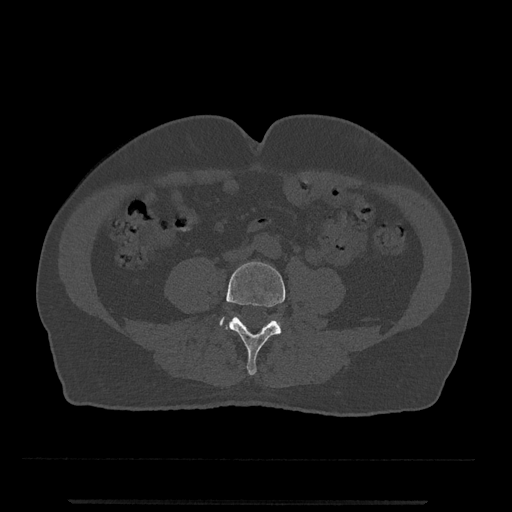
CT including the spine, one axial slice. Slice 126 of 797 in the series (ordered by position). 120 kVp. Bone window (W 1800 / L 400 HU). 512 × 512 image matrix, field of view 419 × 419 mm. Male patient, age 63 years. Case-level facts recorded for this patient, not image findings: primary cancer: prostate.
Annotated regions visible in this slice (semi-automatic segmentation, software-assisted and operator-edited):
- L4 vertebra: bounding box <226,261,286,375> (left, top, right, bottom; pixels)
- L5 vertebra: <220,317,281,327>